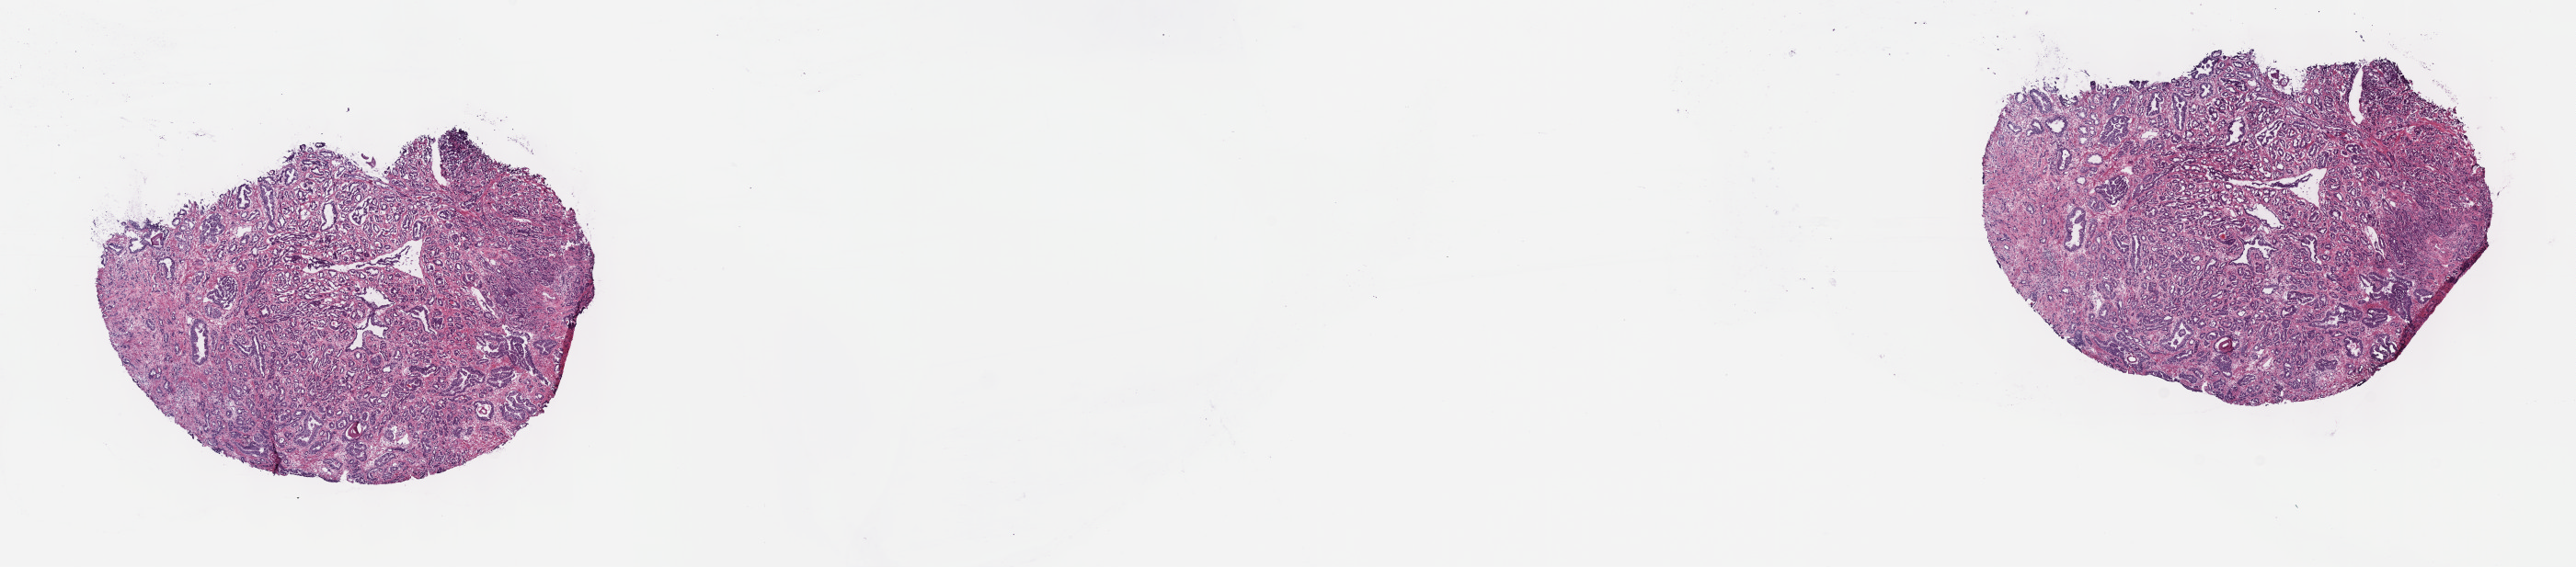
Digitized H&E tissue section (whole slide) — low-resolution overview of the scanned area, about 22.7 x 5.0 mm; frozen section; primary tumour sample from the prostate. Male patient; age at initial diagnosis 51 years. Gleason score: 7 (4+3). Pathologist review of this section (percent, as recorded): tumour cells 70%, tumour nuclei 80%, normal cells 10%, stromal cells 20%, necrosis 0%. Inflammatory infiltration, as recorded: lymphocyte infiltration 0%, monocyte infiltration 0%, neutrophil infiltration 0%.
Lymph nodes positive (case pathology): 0 of 4 examined. Laterality: bilateral. Diagnosis: Adenocarcinoma, NOS (prostate gland).